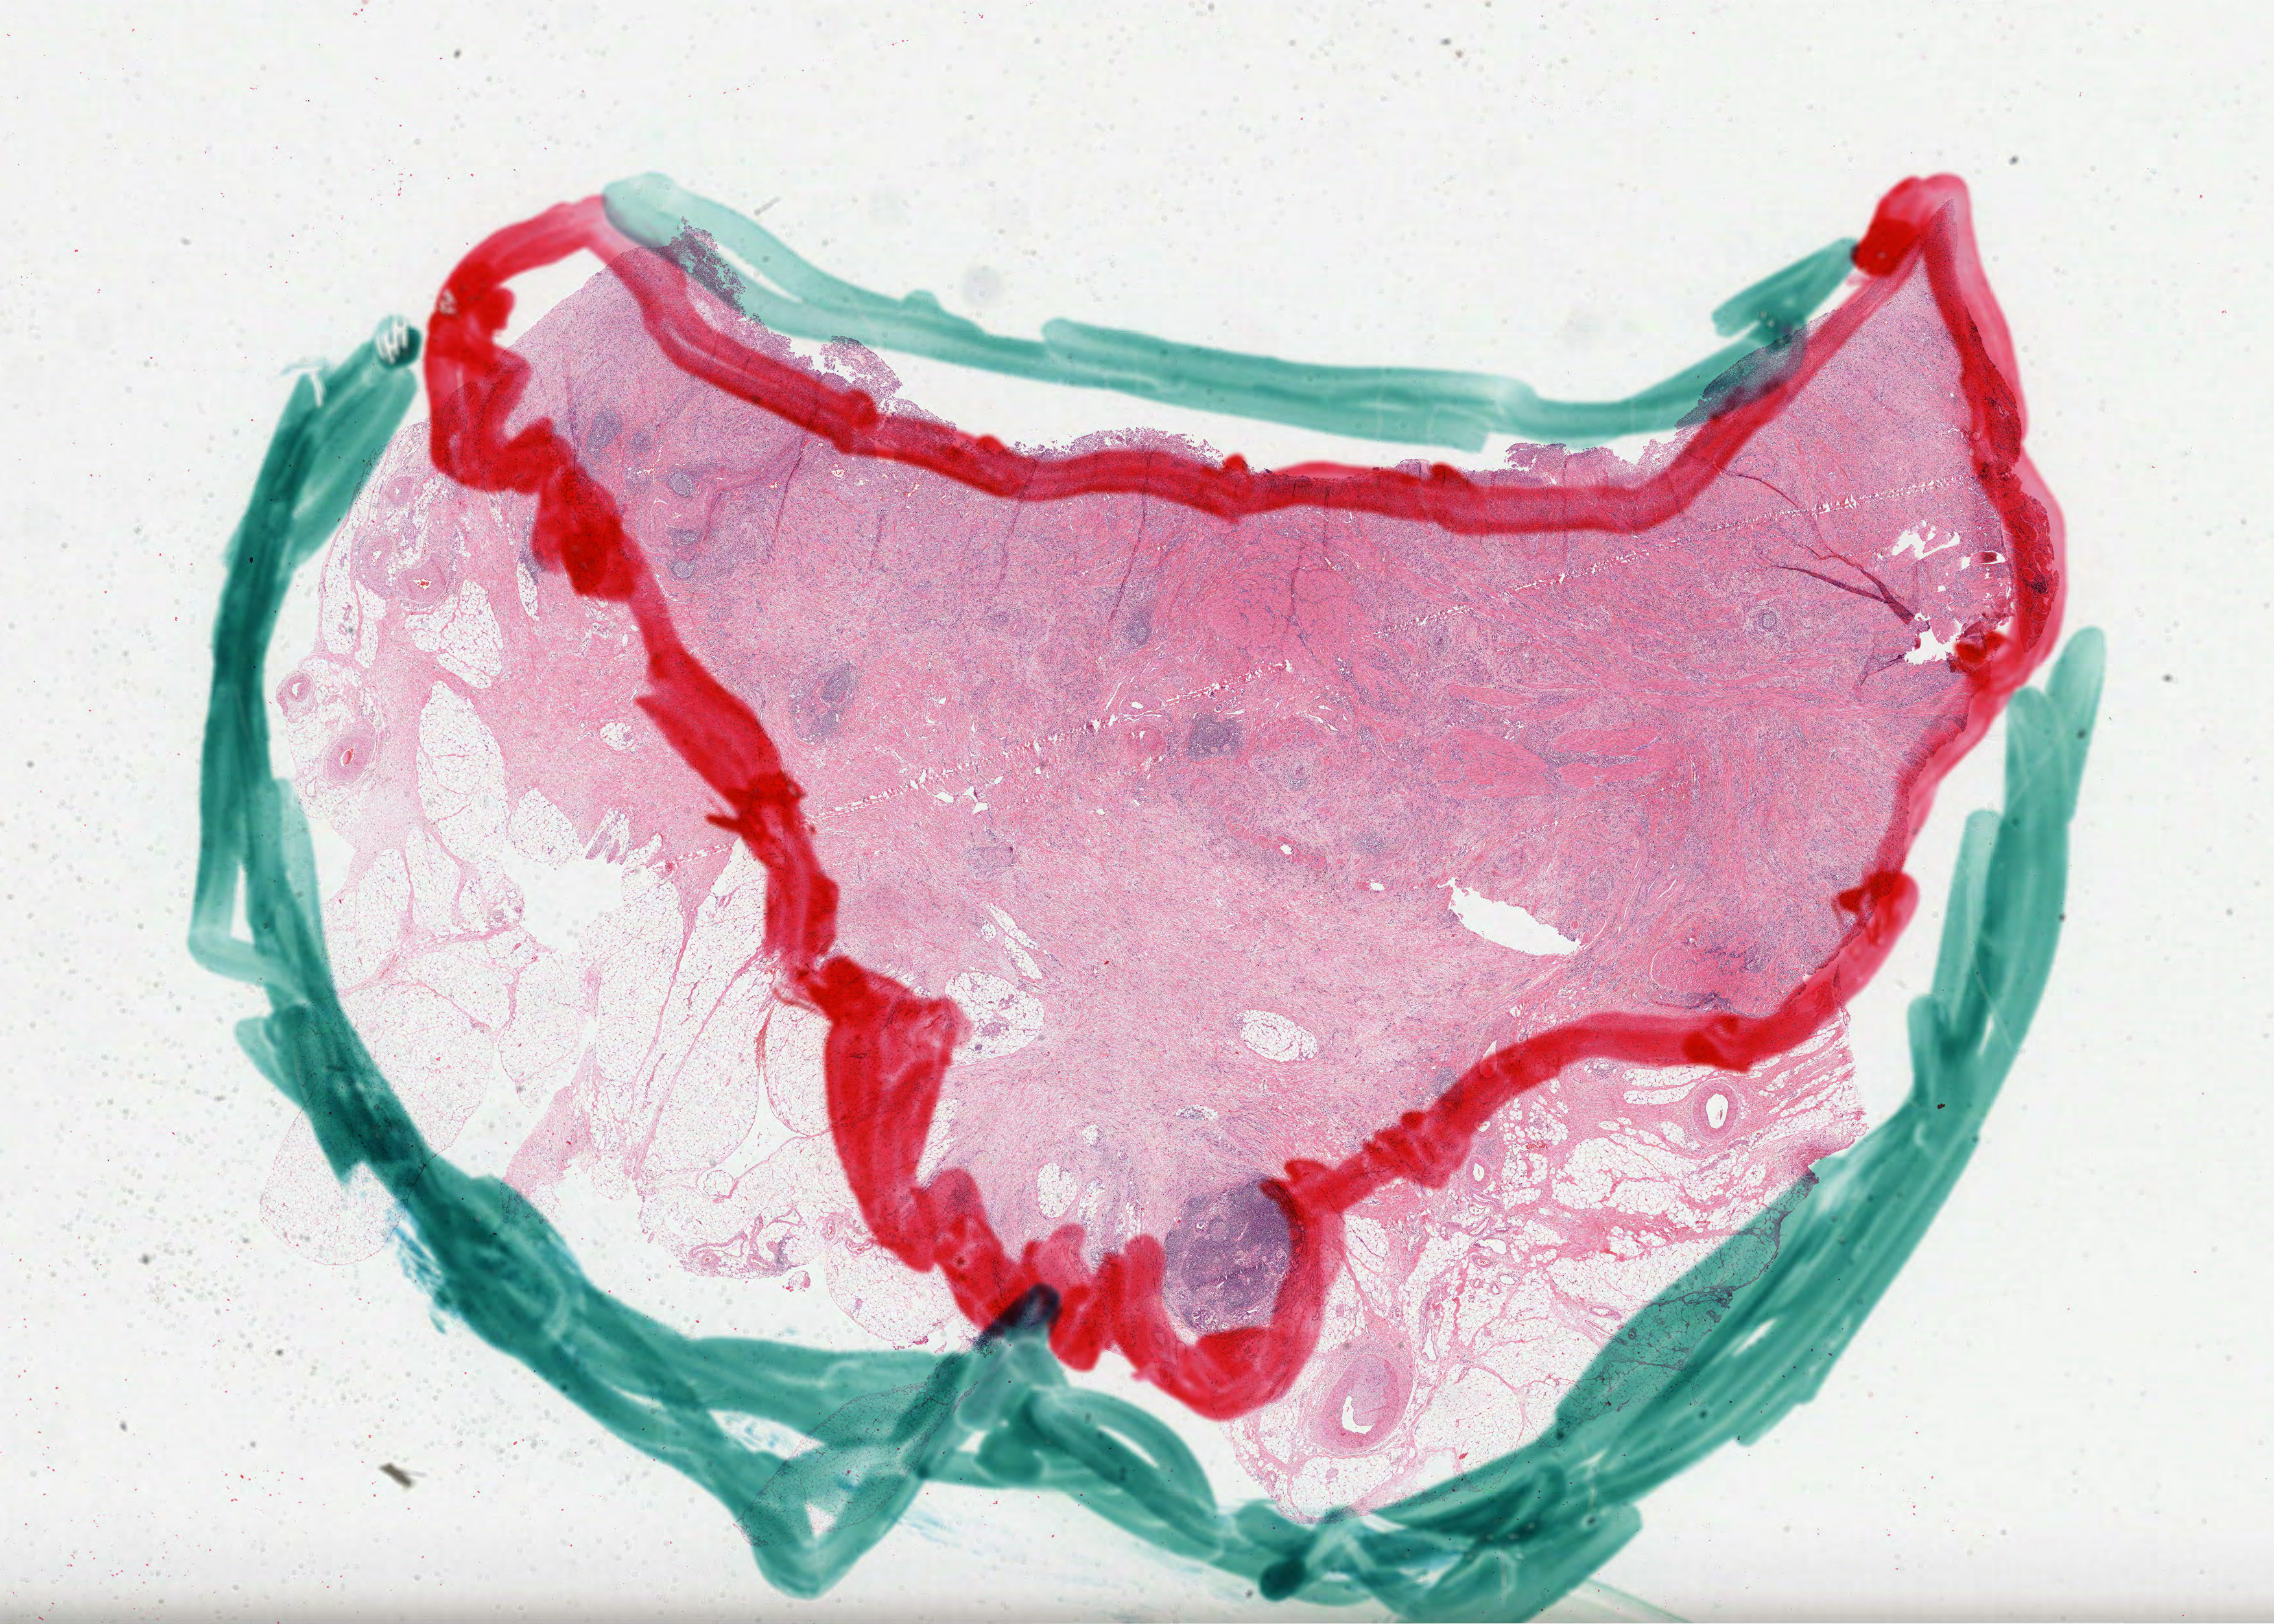
Digitized H&E tissue section (whole slide), whole scanned area (about 28.3 x 20.2 mm) shown as a low-resolution overview, formalin-fixed paraffin-embedded (FFPE) diagnostic section, primary tumour sample from the stomach. Patient: female, age at initial diagnosis 68 years. Histologic grade: G3 (poorly differentiated).
- diagnosis: Adenocarcinoma, NOS
- AJCC pathologic stage: IIIB